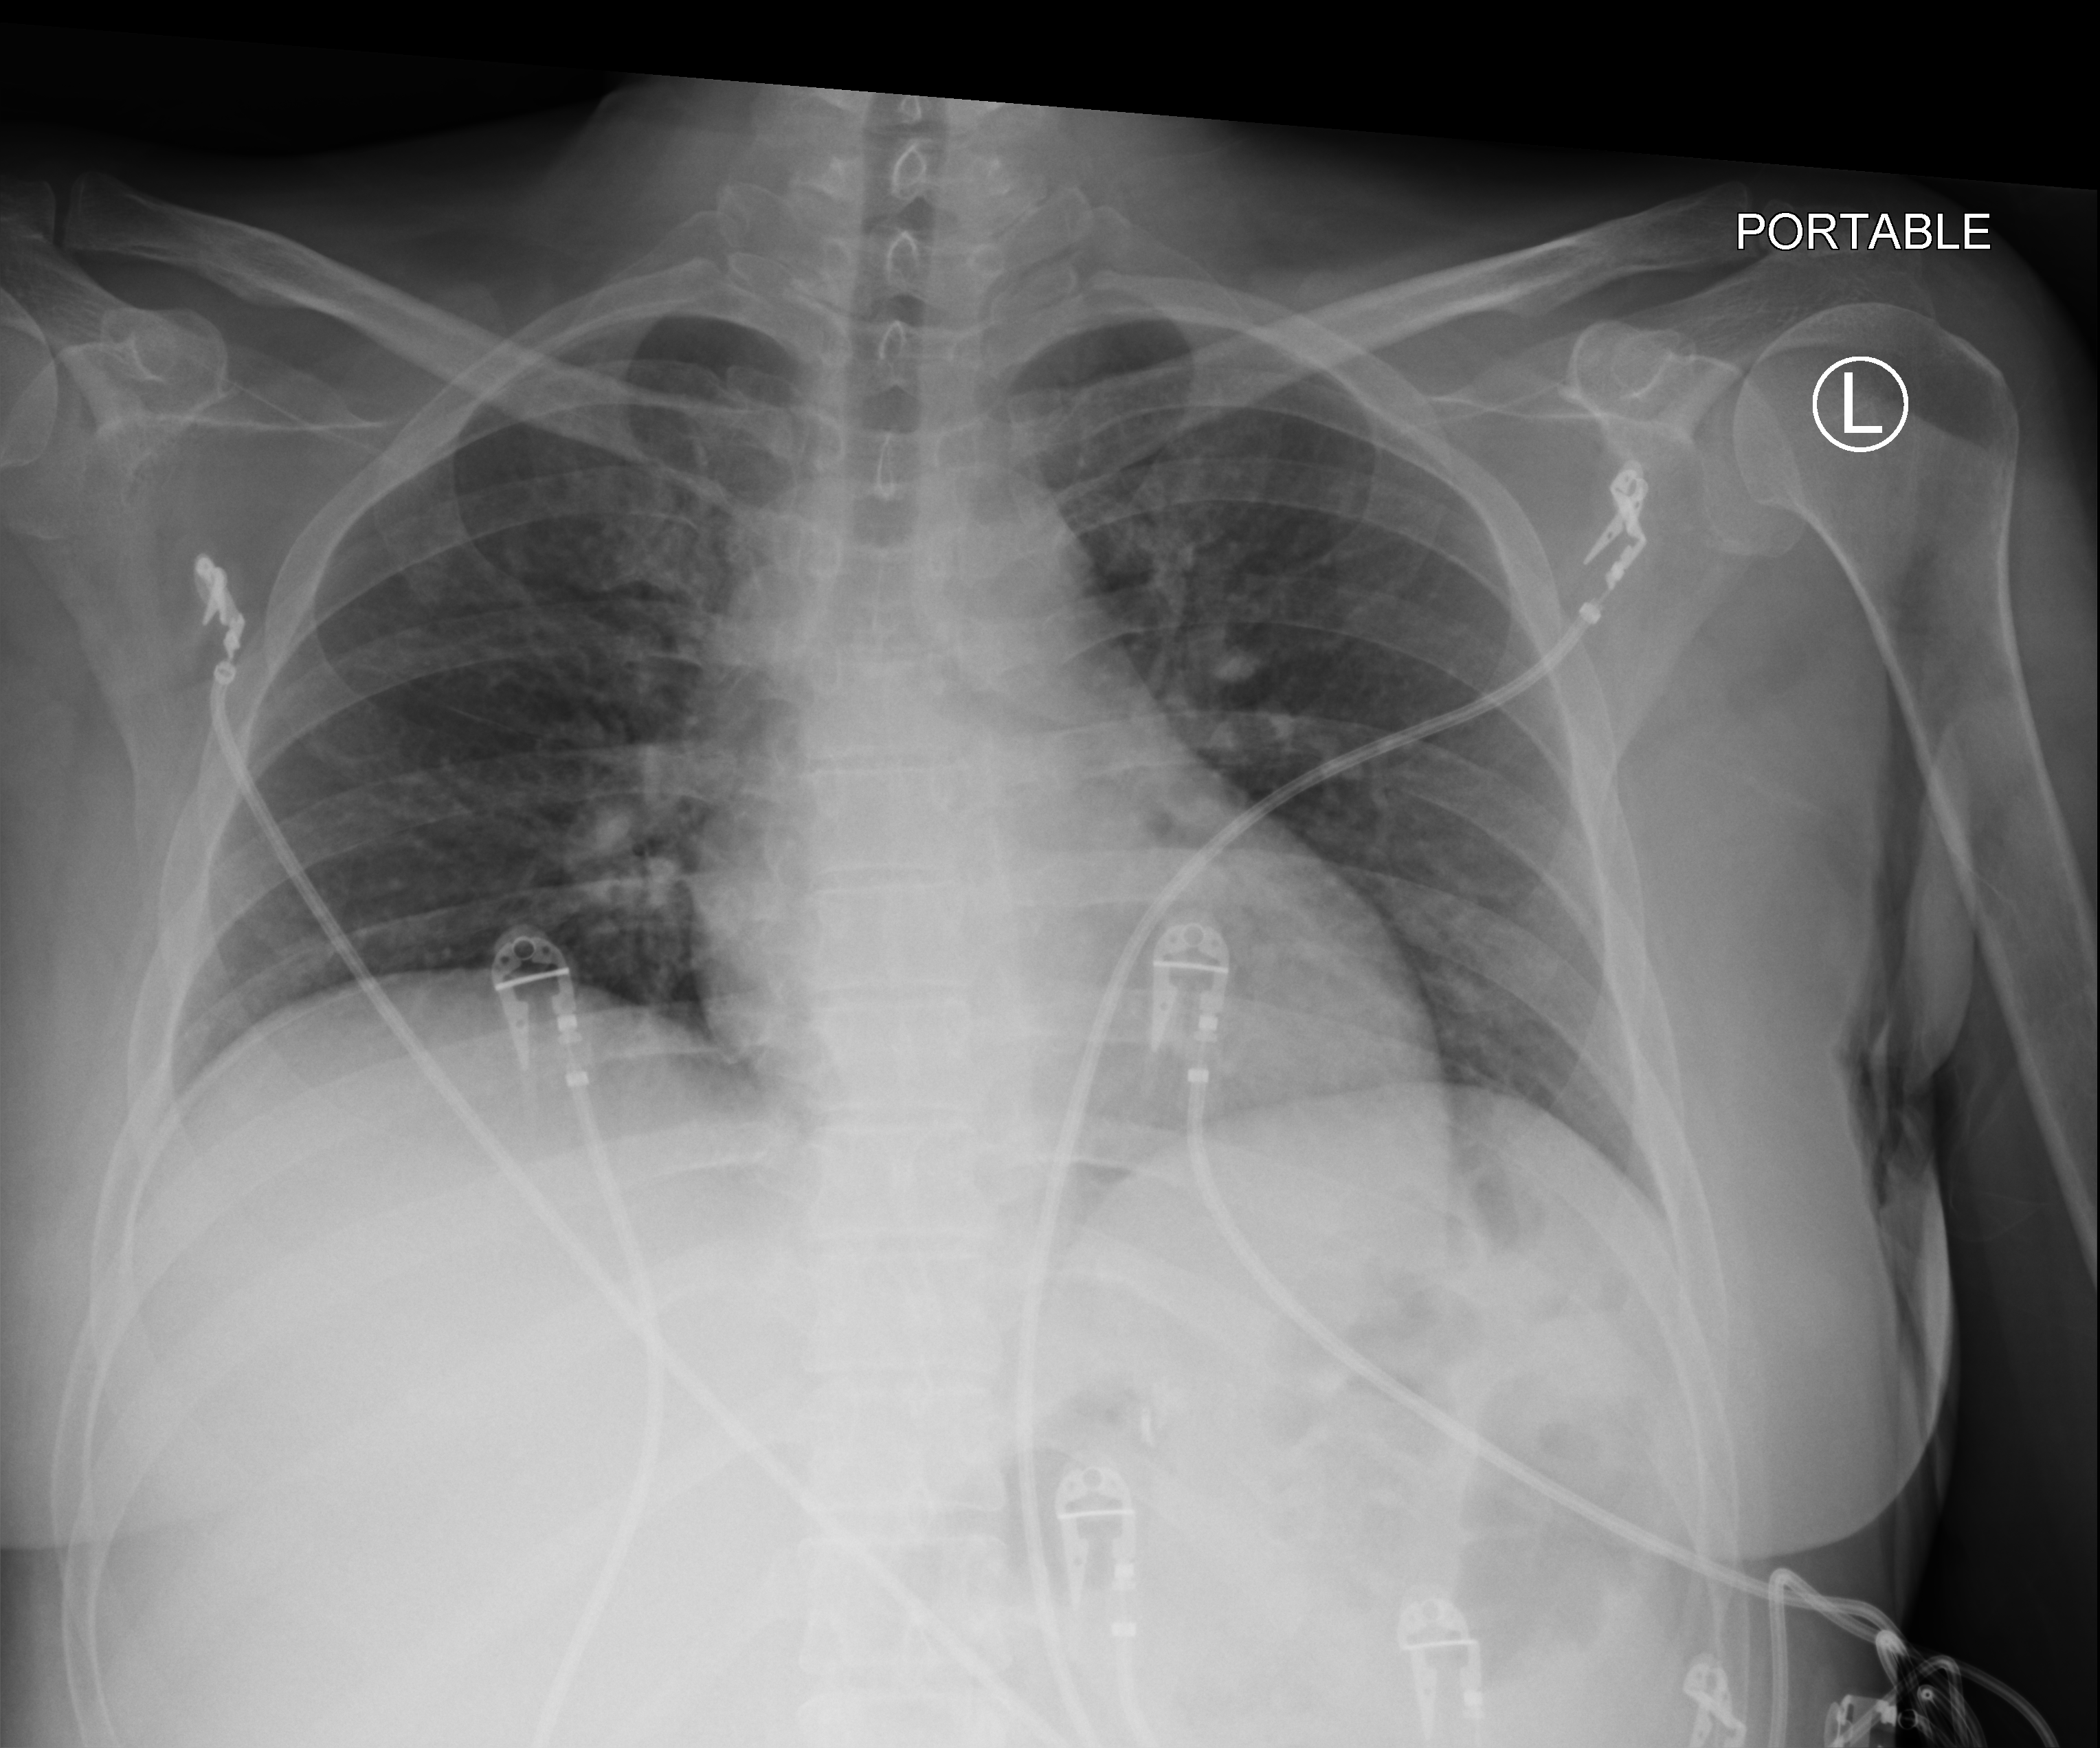
Bedside chest radiograph (computed radiography), anteroposterior (AP) projection. Patient hospitalised with COVID-19; female, aged 18–59 years.
From the hospital-stay record, not from the radiograph (when in the stay this image was taken is not recorded): admitted to intensive care during this hospital stay: no; mechanically ventilated during this hospital stay: no.